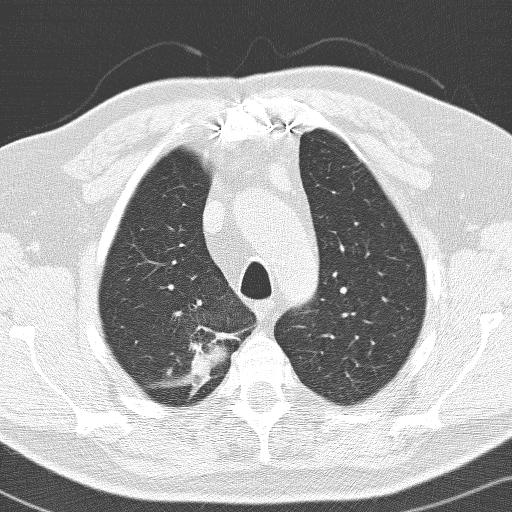
Chest CT (low-dose screening protocol), one axial image, baseline screening round, lung window (W 1500 / L -600 HU), lung (sharp) reconstruction kernel (D). Male, age 66 years at enrolment.
Lesion marked by an expert reader, bounding box [x1, y1, x2, y2] px = [154, 315, 231, 393]. Reader record for this screening exam (exam-level; its link to the box is not recorded): non-calcified nodule or mass ≥4 mm, right upper lobe, 36 × 30 mm, spiculated (stellate) margins, soft tissue attenuation. Official screen result: positive, change unspecified: nodule(s) >= 4 mm or enlarging nodule(s), mass(es), or other non-specific abnormalities suspicious for lung cancer. Participant outcome: lung cancer diagnosed 103 days after this screen — adenocarcinoma, NOS, right upper lobe, poorly differentiated (G3), stage IIB (AJCC 6th edition), 33 mm at pathology.